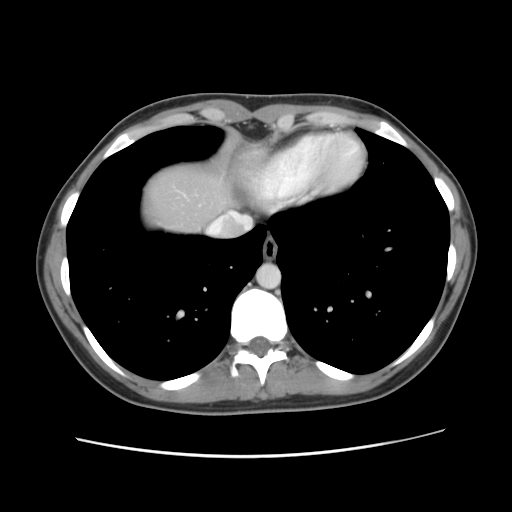
Contrast-enhanced abdominal CT, one axial slice; slice 116 of 134 in the series (ordered by position); 120 kVp; intravenous contrast given; soft-tissue window (W 400 / L 40 HU); 2.5 mm slice thickness; 512 × 512 image matrix. Female patient, age 33 years. Case-level facts recorded for this patient, not image findings: diagnosis: colorectal cancer liver metastases, imaged before liver resection; multiple liver metastases: yes; largest metastasis: 4.5 cm.
Annotated regions visible in this slice (manually delineated by an expert):
- liver: bounding box (x1, y1, x2, y2) in pixels: (140, 162, 237, 234)
- planned liver remnant (the part of the liver to remain after resection): (140, 161, 237, 235)